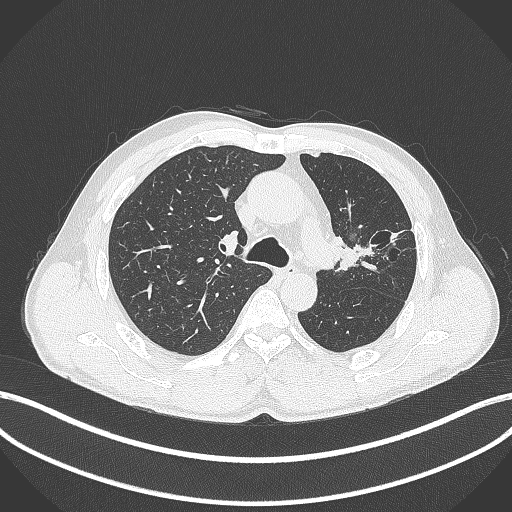
Chest CT, one axial slice; slice 281 of 429 in the series (ordered by position); reconstruction kernel B70f; 120 kVp; lung window (W 1500 / L -600 HU); 1 mm slice thickness; 512 × 512 image matrix, field of view 400 × 400 mm. Patient: male, 57 years. Case-level facts recorded for this patient, not image findings: clinical TNM (as recorded): T2b N0 M0.
Annotated regions visible in this slice (rectangle marked by the reading radiologist):
- lung tumour (recorded histology: squamous cell carcinoma): bounding box (x1, y1, x2, y2) in pixels: (336, 236, 380, 278)